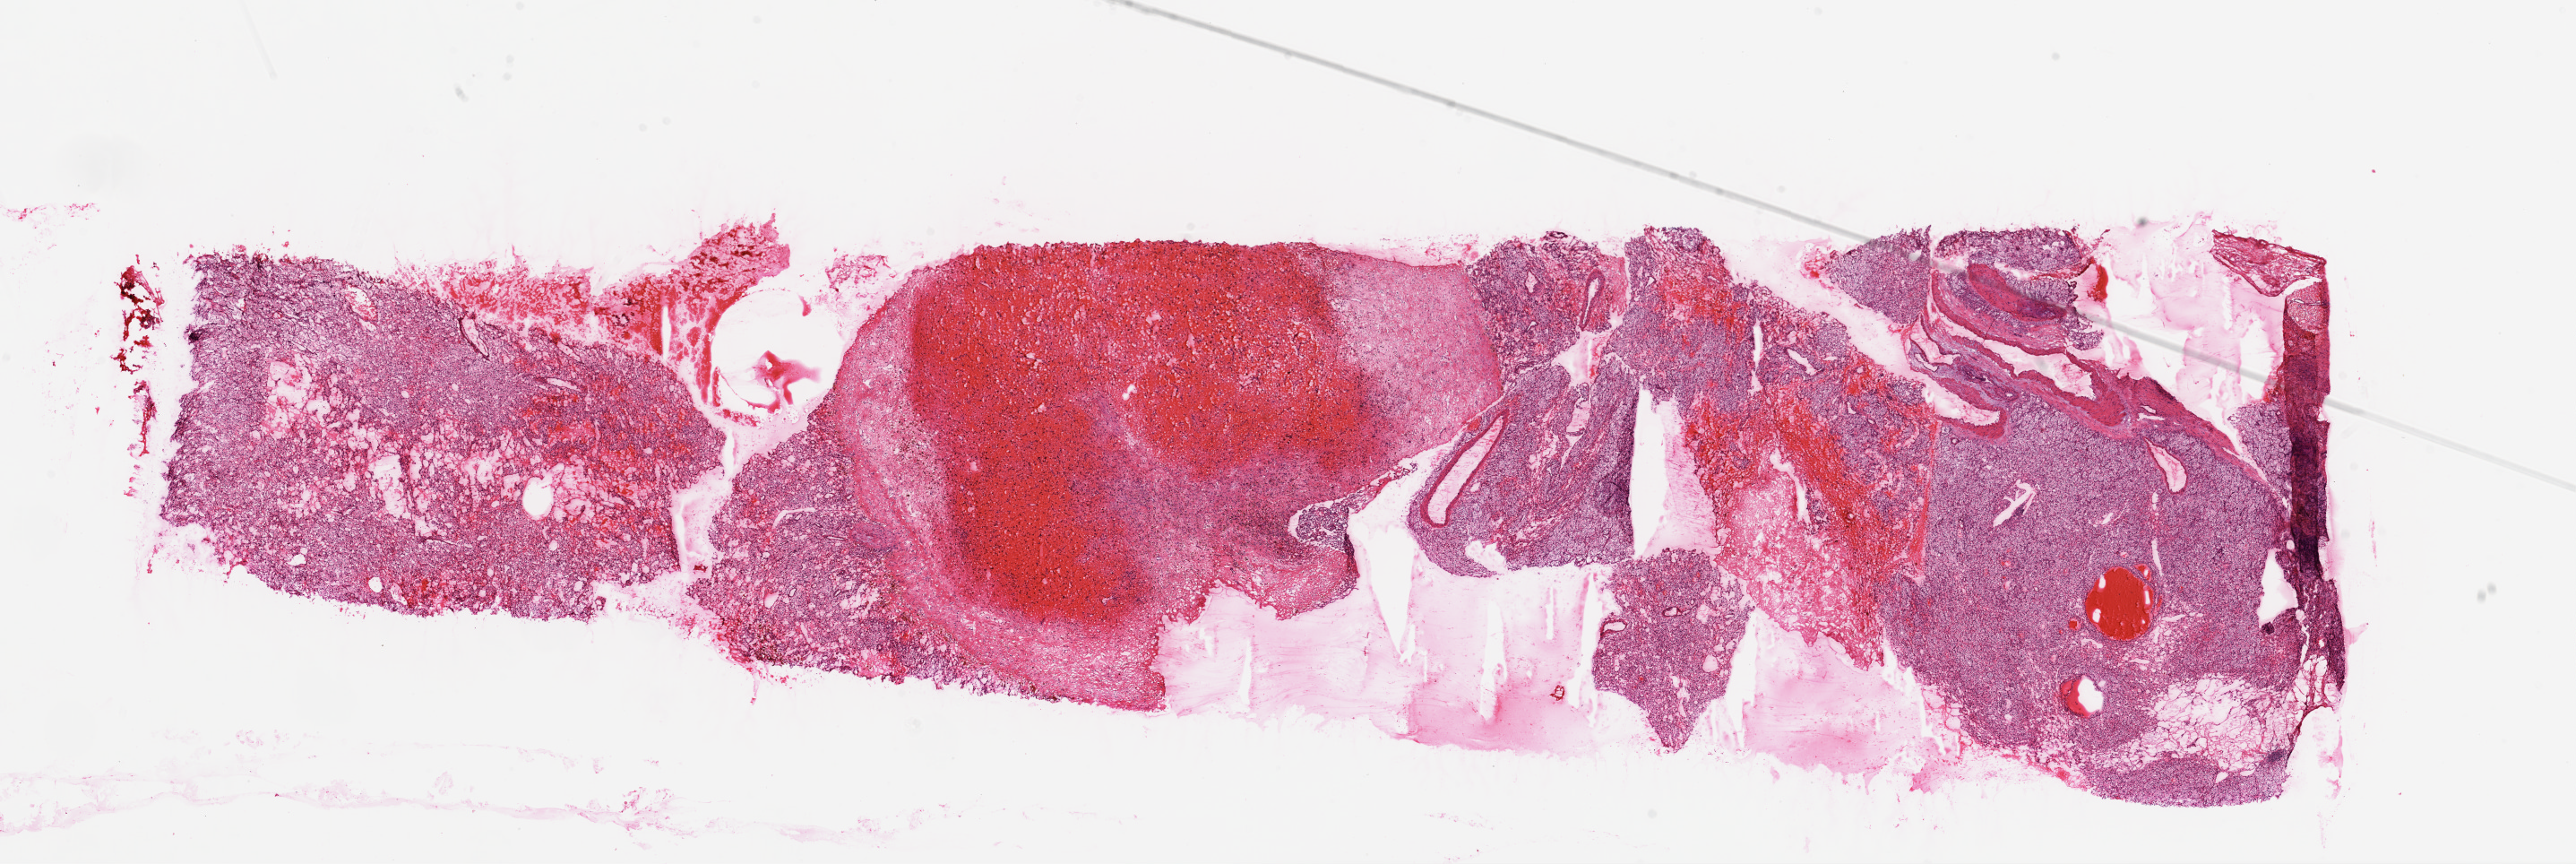
Digitized H&E-stained tissue section (whole slide), a low-resolution overview of the entire scanned area, about 23.1 x 7.7 mm. Frozen section from the top of the tissue portion. Kidney, primary tumour sample. Male patient; age at initial diagnosis 42 years. Histologic grade: G2 (moderately differentiated). Slide review estimates, as recorded: tumour cells 75%, tumour nuclei 80%, normal cells 0%, stromal cells 25%, necrosis 0%.
AJCC pathologic stage: I. Histologic diagnosis: Clear cell adenocarcinoma, NOS. TNM: T1b NX M0.